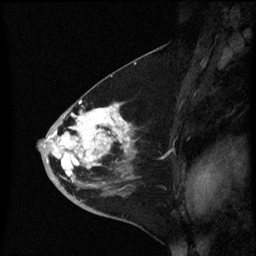
Breast MRI (dynamic contrast-enhanced), one sagittal slice. Slice 31 of 60 in the series (ordered by position). Dynamic contrast-enhanced series, image 2 of 3 at this slice position (ordered by acquisition). 1.5 T. TE 4.2 ms, TR 8.4 ms. 2.3 mm slice thickness. 256 × 256 image matrix, field of view 200 × 200 mm. Patient: female, 46 years. Case-level facts recorded for this patient, not image findings: setting: breast cancer imaged before/during neoadjuvant chemotherapy; receptor status: HER2-positive.
Annotated regions visible in this slice (semi-automatic segmentation, software-assisted and operator-edited):
- analysis volume of interest (the breast-tissue region the enhancement analysis was run in; not a lesion): box from (x=39, y=96) to (x=139, y=187) px
- tumour enhancement mask (voxels above the 70 % enhancement threshold inside the analysis volume of interest): (x=43, y=102)–(x=130, y=181)